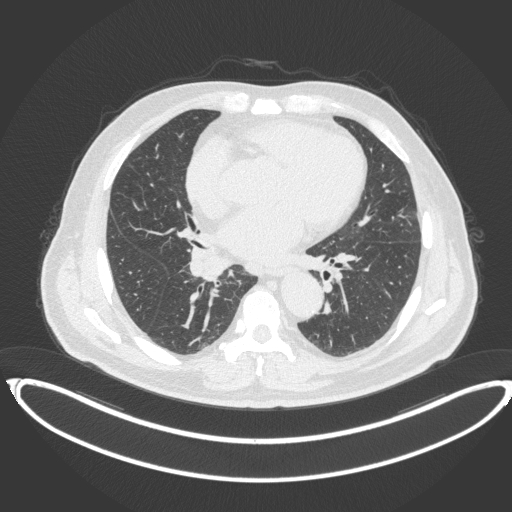
Chest CT, one axial slice; position 194 of 383 along the scan axis; reconstruction kernel B31f; lung window (W 1500 / L -600 HU); 512 × 512 image matrix, field of view 448 × 448 mm. Patient: male, 61 years. Case-level facts recorded for this patient, not image findings: clinical TNM (as recorded): T1b N1 M0.
Annotated regions visible in this slice (bounding box drawn by a radiologist):
- lung tumour (recorded histology: squamous cell carcinoma): bounding box [x1, y1, x2, y2] px = [189, 241, 233, 283]